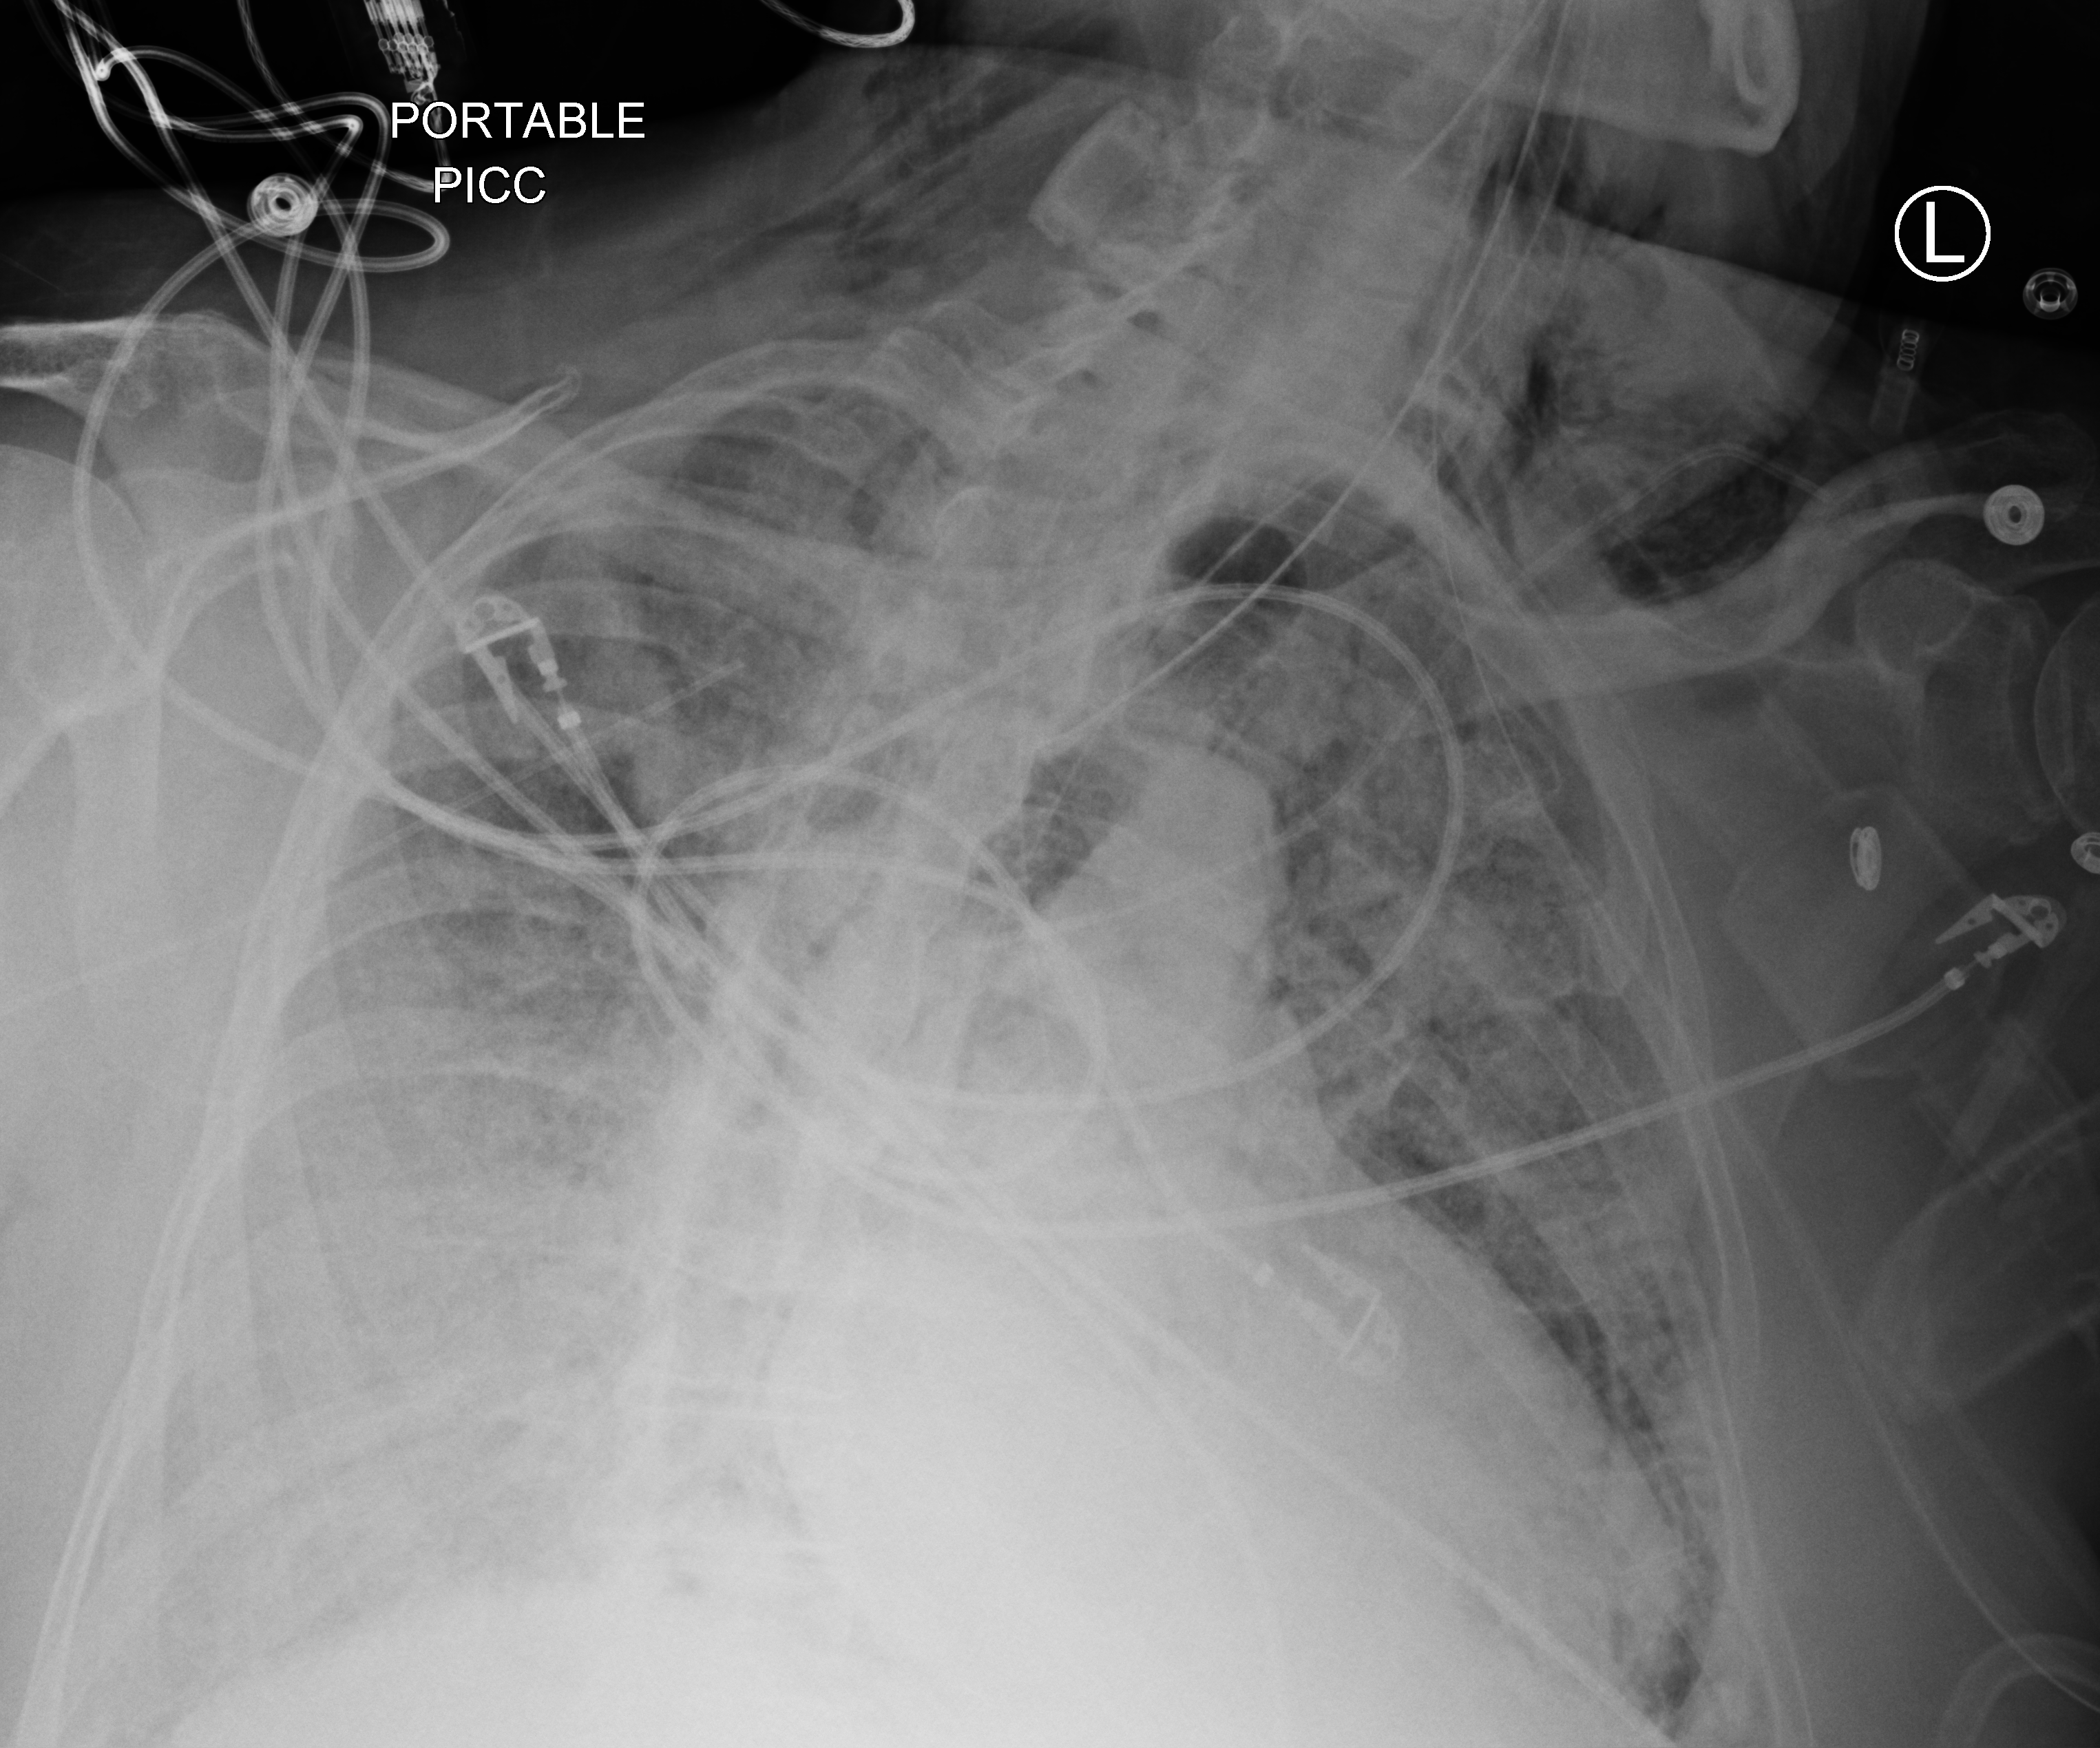
Portable chest radiograph, anteroposterior (AP) projection. Male patient hospitalised with COVID-19, age 75–90 years.
Admission-level facts for this patient (not findings on this image; timing relative to this image not recorded): other chronic lung disease (admission record): no; admitted to intensive care during this hospital stay: yes.